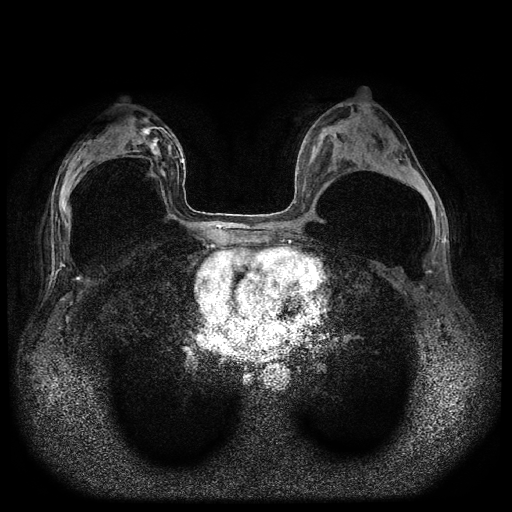
Breast MRI (dynamic contrast-enhanced, multi-phase), one axial slice. Slice 46 of 116 in the series (ordered by position). Dynamic contrast-enhanced series, time point 2 of 5 at this slice position (early post-contrast). 1.5 T. TE 2.6 ms, TR 5.4 ms. 2 mm slice thickness. 512 × 512 image matrix, field of view 340 × 340 mm. Patient: female, 42 years.
Annotated regions visible in this slice (semi-automatic segmentation, software-assisted and operator-edited):
- breast lesion (labelled 'tumour' in the annotation; benign lesions carry a separate 'benign' label): box from (x=140, y=127) to (x=159, y=154) px